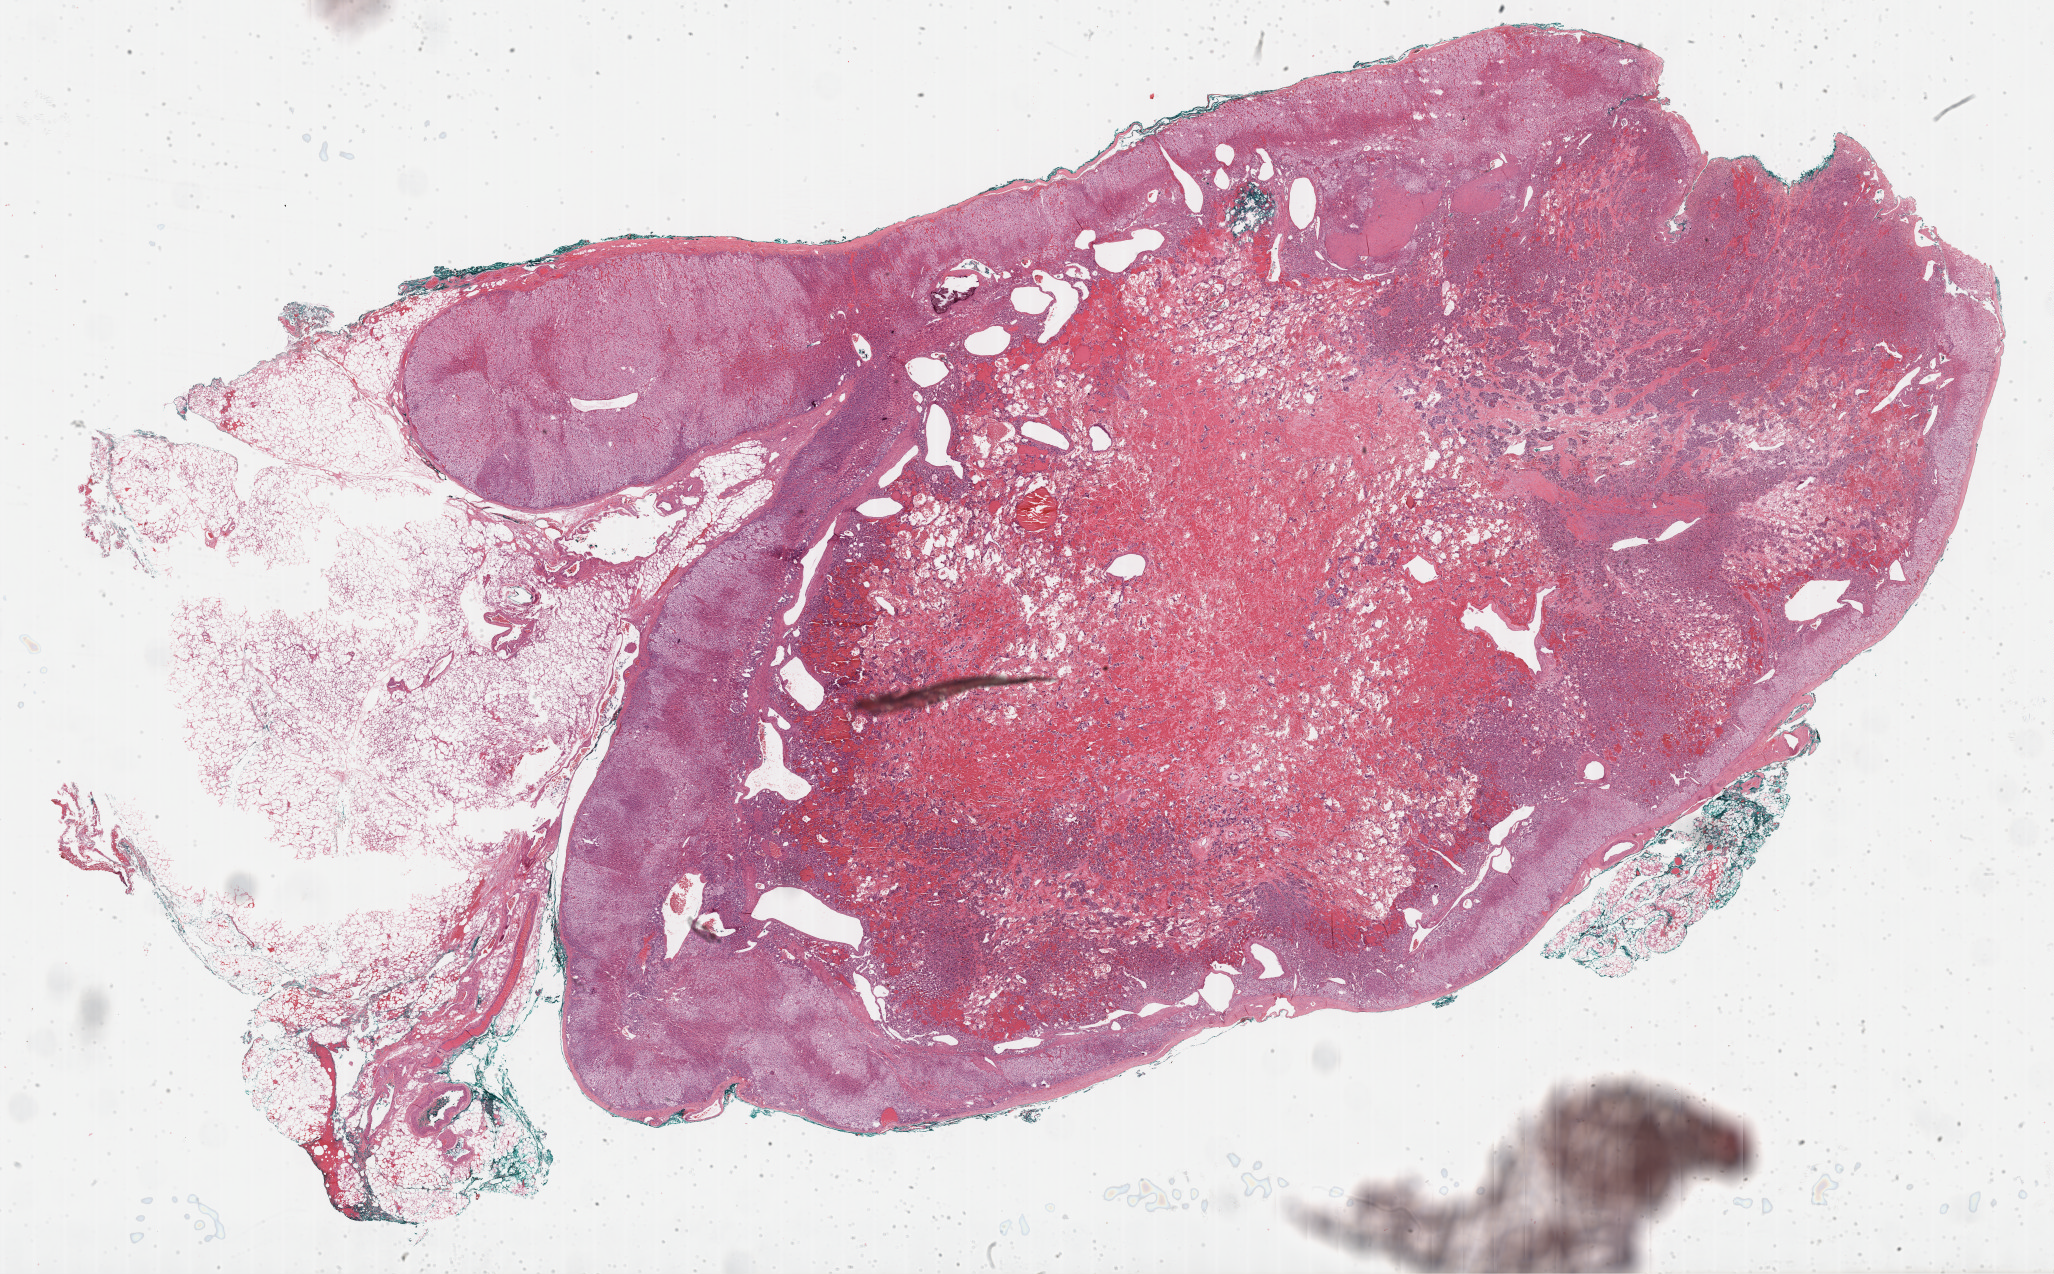
H&E whole-slide image, a low-resolution overview of the entire scanned area, about 33.2 x 20.6 mm (acquisition: 40x scan); formalin-fixed paraffin-embedded (FFPE) diagnostic section; primary tumour sample from the adrenal gland. Patient: male, age at initial diagnosis 47 years.
- laterality: right
- diagnosis: Pheochromocytoma, NOS